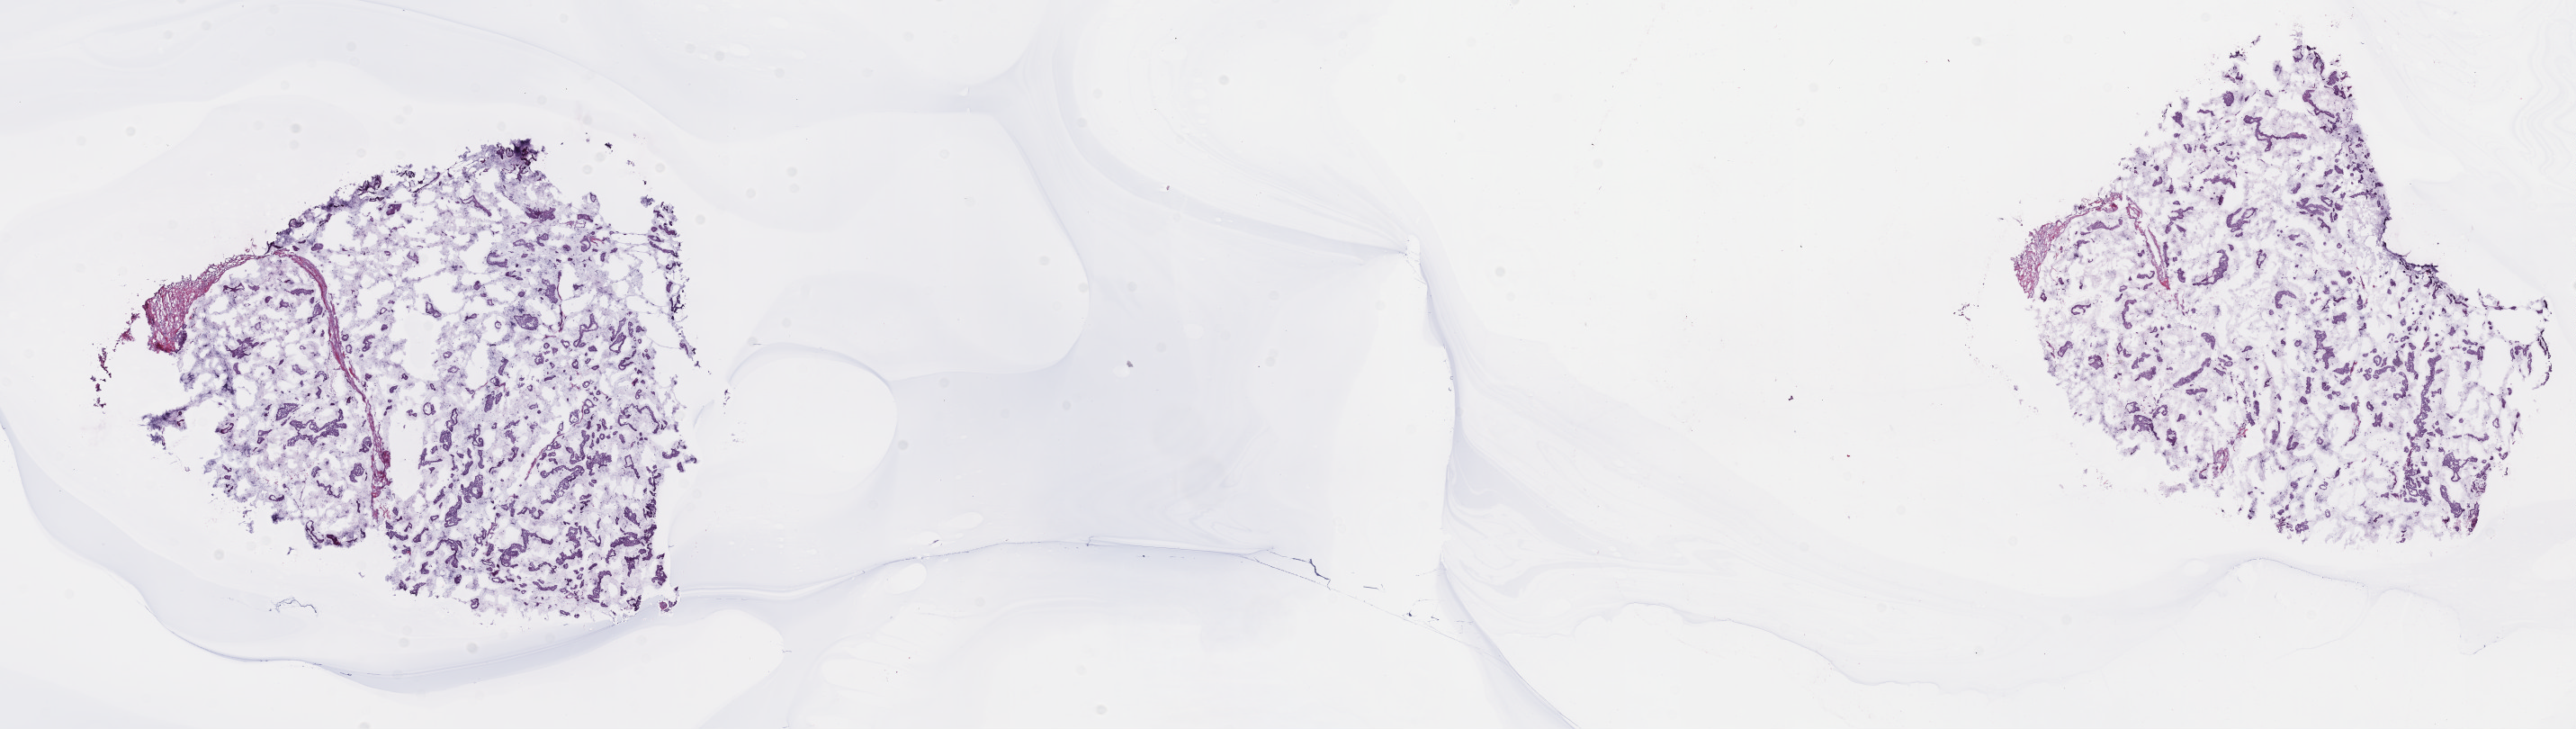
Digitized Hematoxylin and eosin (H&E) stained tissue section (whole slide) — whole scanned area (about 23.2 x 6.6 mm) shown as a low-resolution overview; frozen section from the top of the tissue portion; primary tumour sample from the breast. Female patient; age at initial diagnosis 75 years. Composition of this section per pathologist review: tumour cells 95%, tumour nuclei 96%, normal cells 0%, stromal cells 5%, necrosis 0%. Inflammatory infiltration, as recorded: lymphocyte infiltration 1%, monocyte infiltration 0%, neutrophil infiltration 0%.
• lymph nodes positive (case pathology): 0 of 2 examined
• AJCC pathologic stage: IA
• diagnosis: Mucinous adenocarcinoma